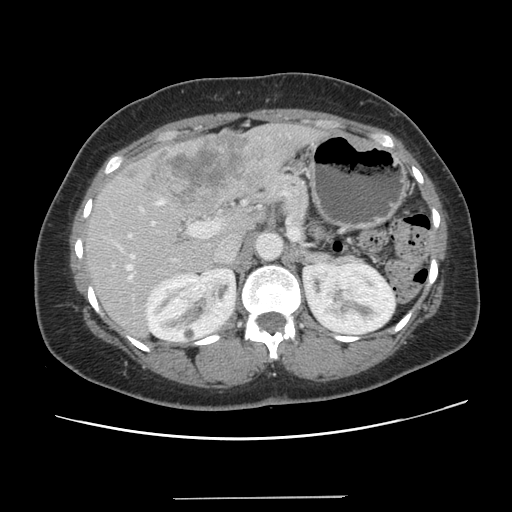
Contrast-enhanced abdominal CT, one axial slice; position 74 of 141 along the scan axis; intravenous contrast given; soft-tissue window (W 400 / L 40 HU); 2.5 mm slice thickness; 512 × 512 image matrix, field of view 366 × 366 mm. Female patient, age 53 years. Case-level facts recorded for this patient, not image findings: diagnosis: colorectal cancer liver metastases, imaged before liver resection; multiple liver metastases: no; largest metastasis: 14.5 cm; disease in both lobes: yes.
Annotated regions visible in this slice (expert manual segmentation):
- hepatic veins: bounding box [x1, y1, x2, y2] px = [126, 254, 134, 279]
- liver: [87, 123, 320, 336]
- planned liver remnant (the part of the liver to remain after resection): [87, 206, 254, 337]
- portal vein (with intrahepatic branches): [128, 200, 222, 238]
- liver metastasis: [141, 134, 251, 203]